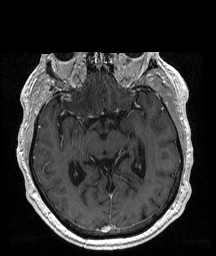
Brain MRI from a brain-tumour surgery series, one axial slice. Slice 111 of 192 in the series (ordered by position). T1-weighted post-contrast. 1 mm slice thickness. 216 × 256 image matrix, field of view 211 × 250 mm. Case-level facts recorded for this patient, not image findings: histopathology: Glioblastoma; WHO grade: 4; IDH mutation: no; tumour location: Right Frontal.
Annotated regions visible in this slice (manually delineated by an expert):
- tumour: bounding box [x1, y1, x2, y2] px = [57, 92, 67, 100]